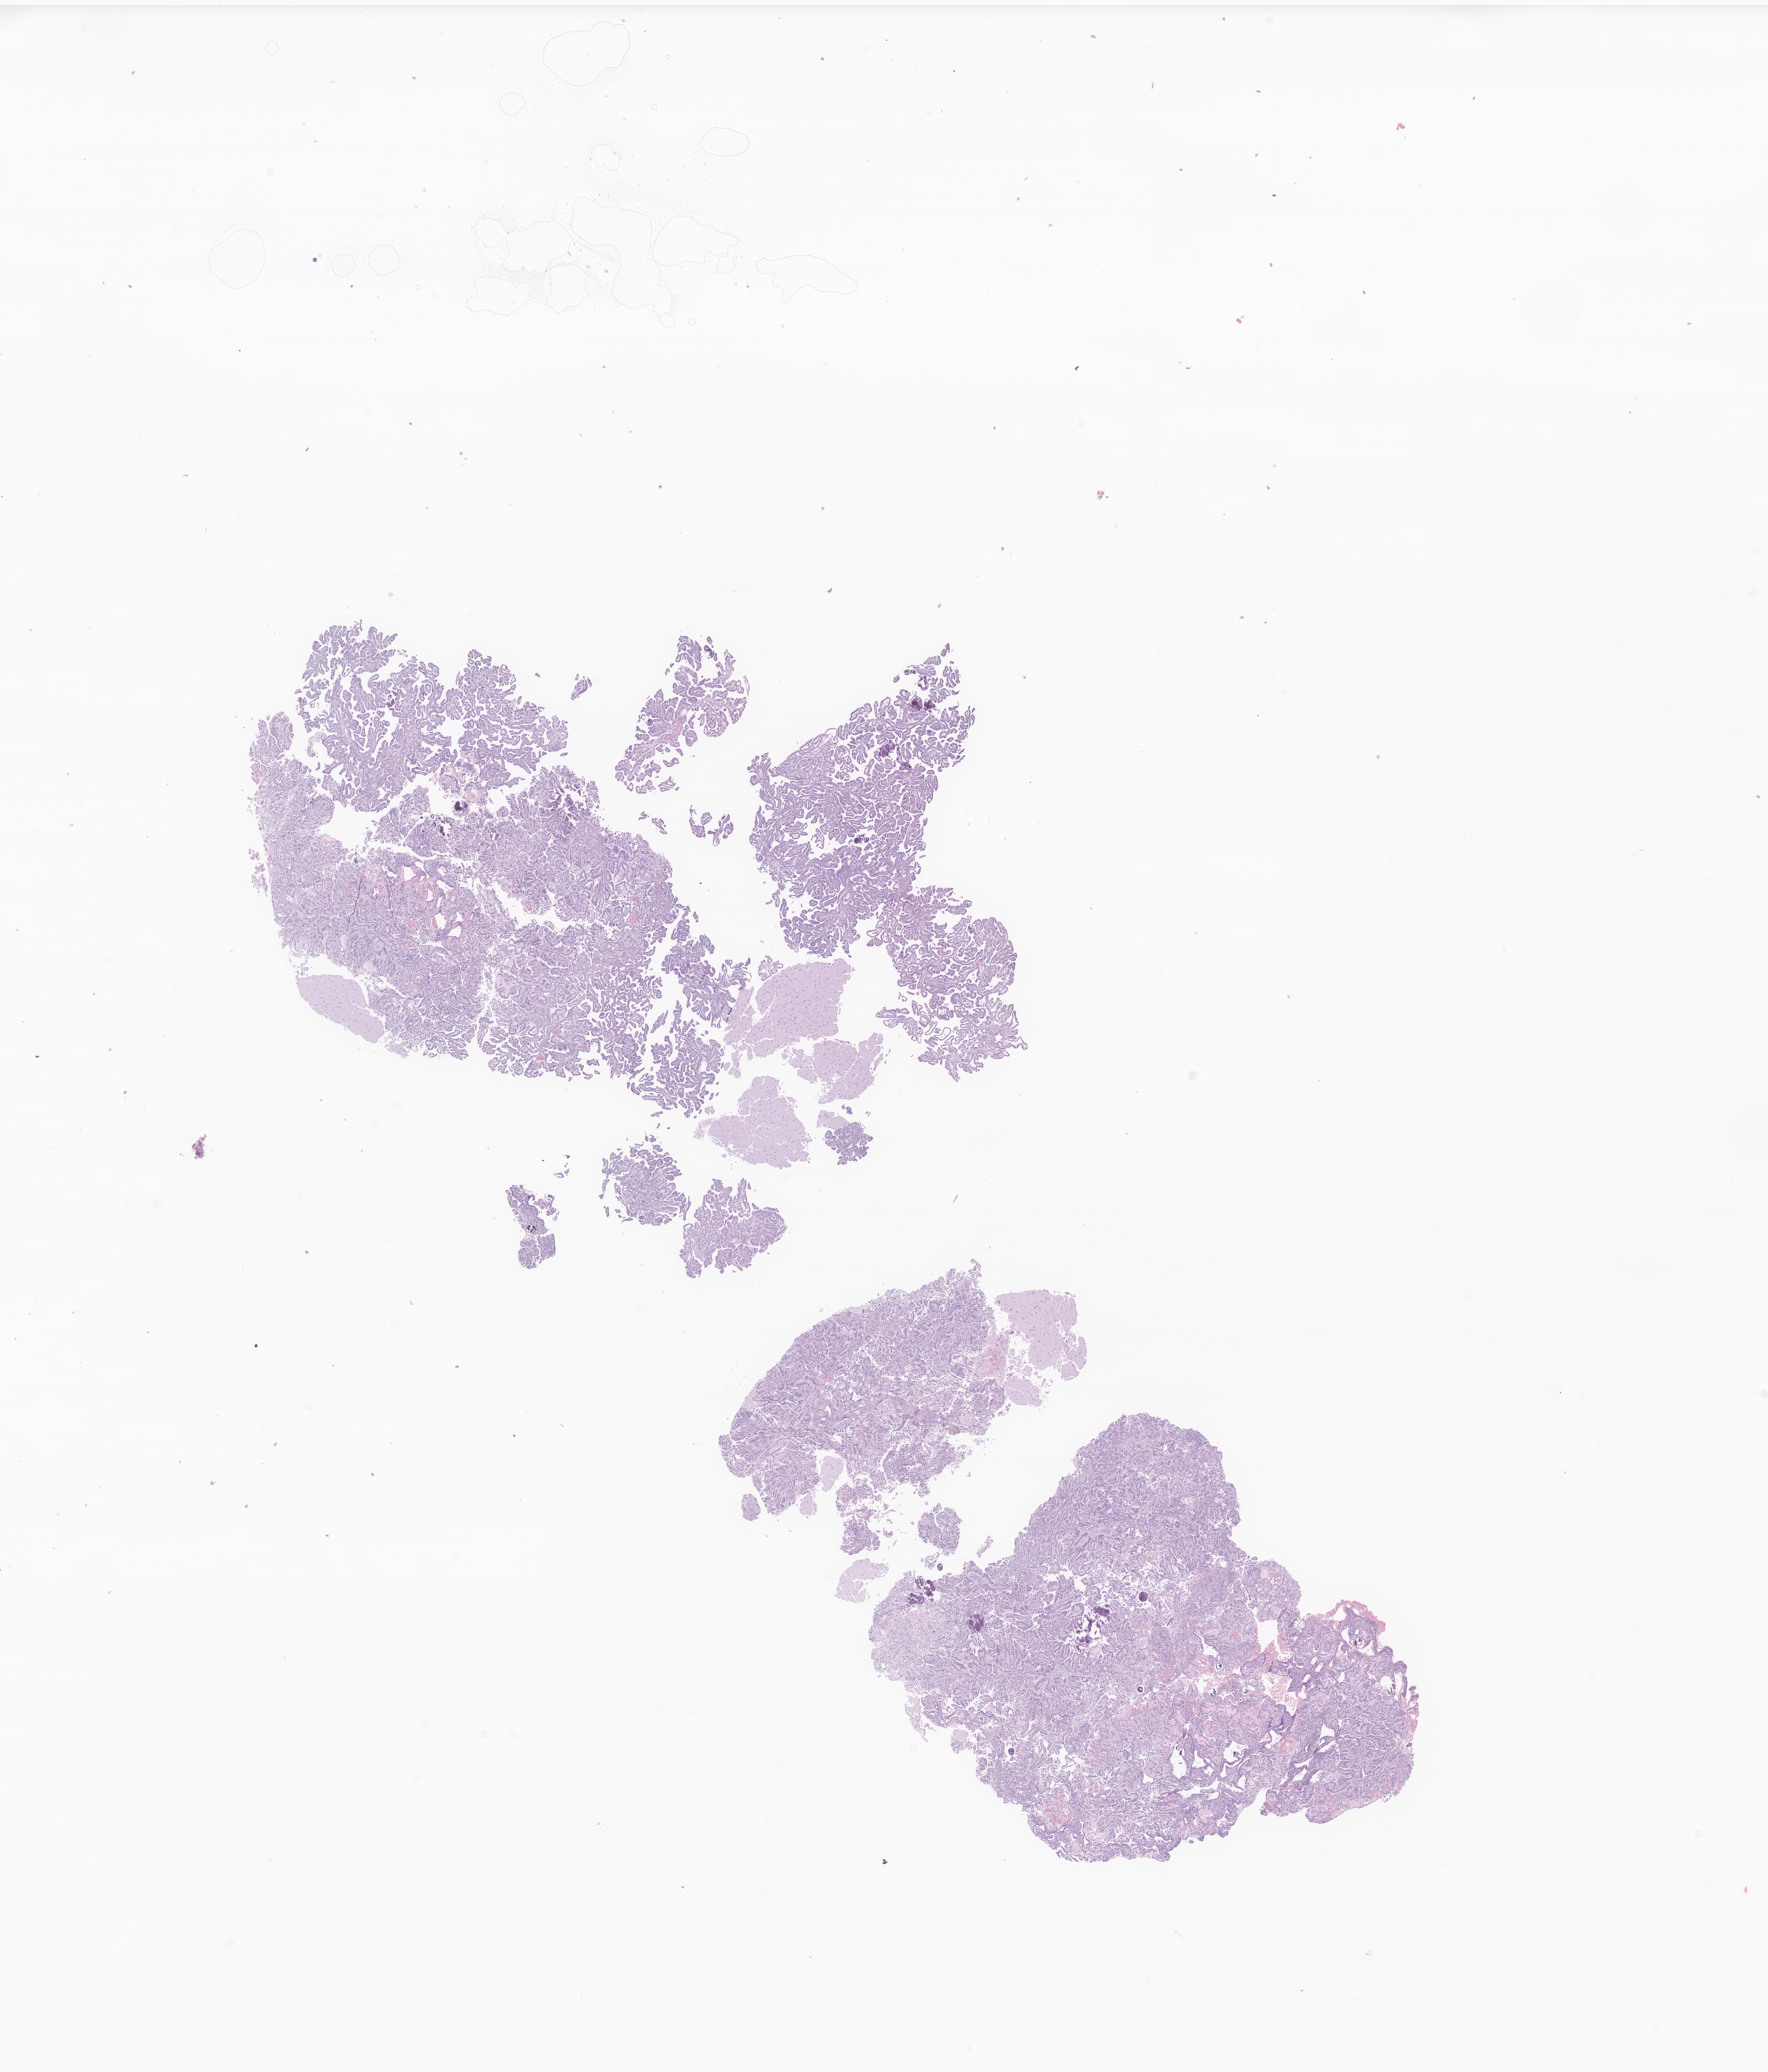
H&E whole-slide image of tumor tissue from the cerebral ventricle, low-resolution overview of the scanned area, about 15.2 x 17.8 mm, formalin-fixed, paraffin-embedded (FFPE) tissue. Patient male; age 750 days (about 2.1 years).
Diagnosis (ICD-O-3 morphology term): Choroid plexus papilloma, NOS.